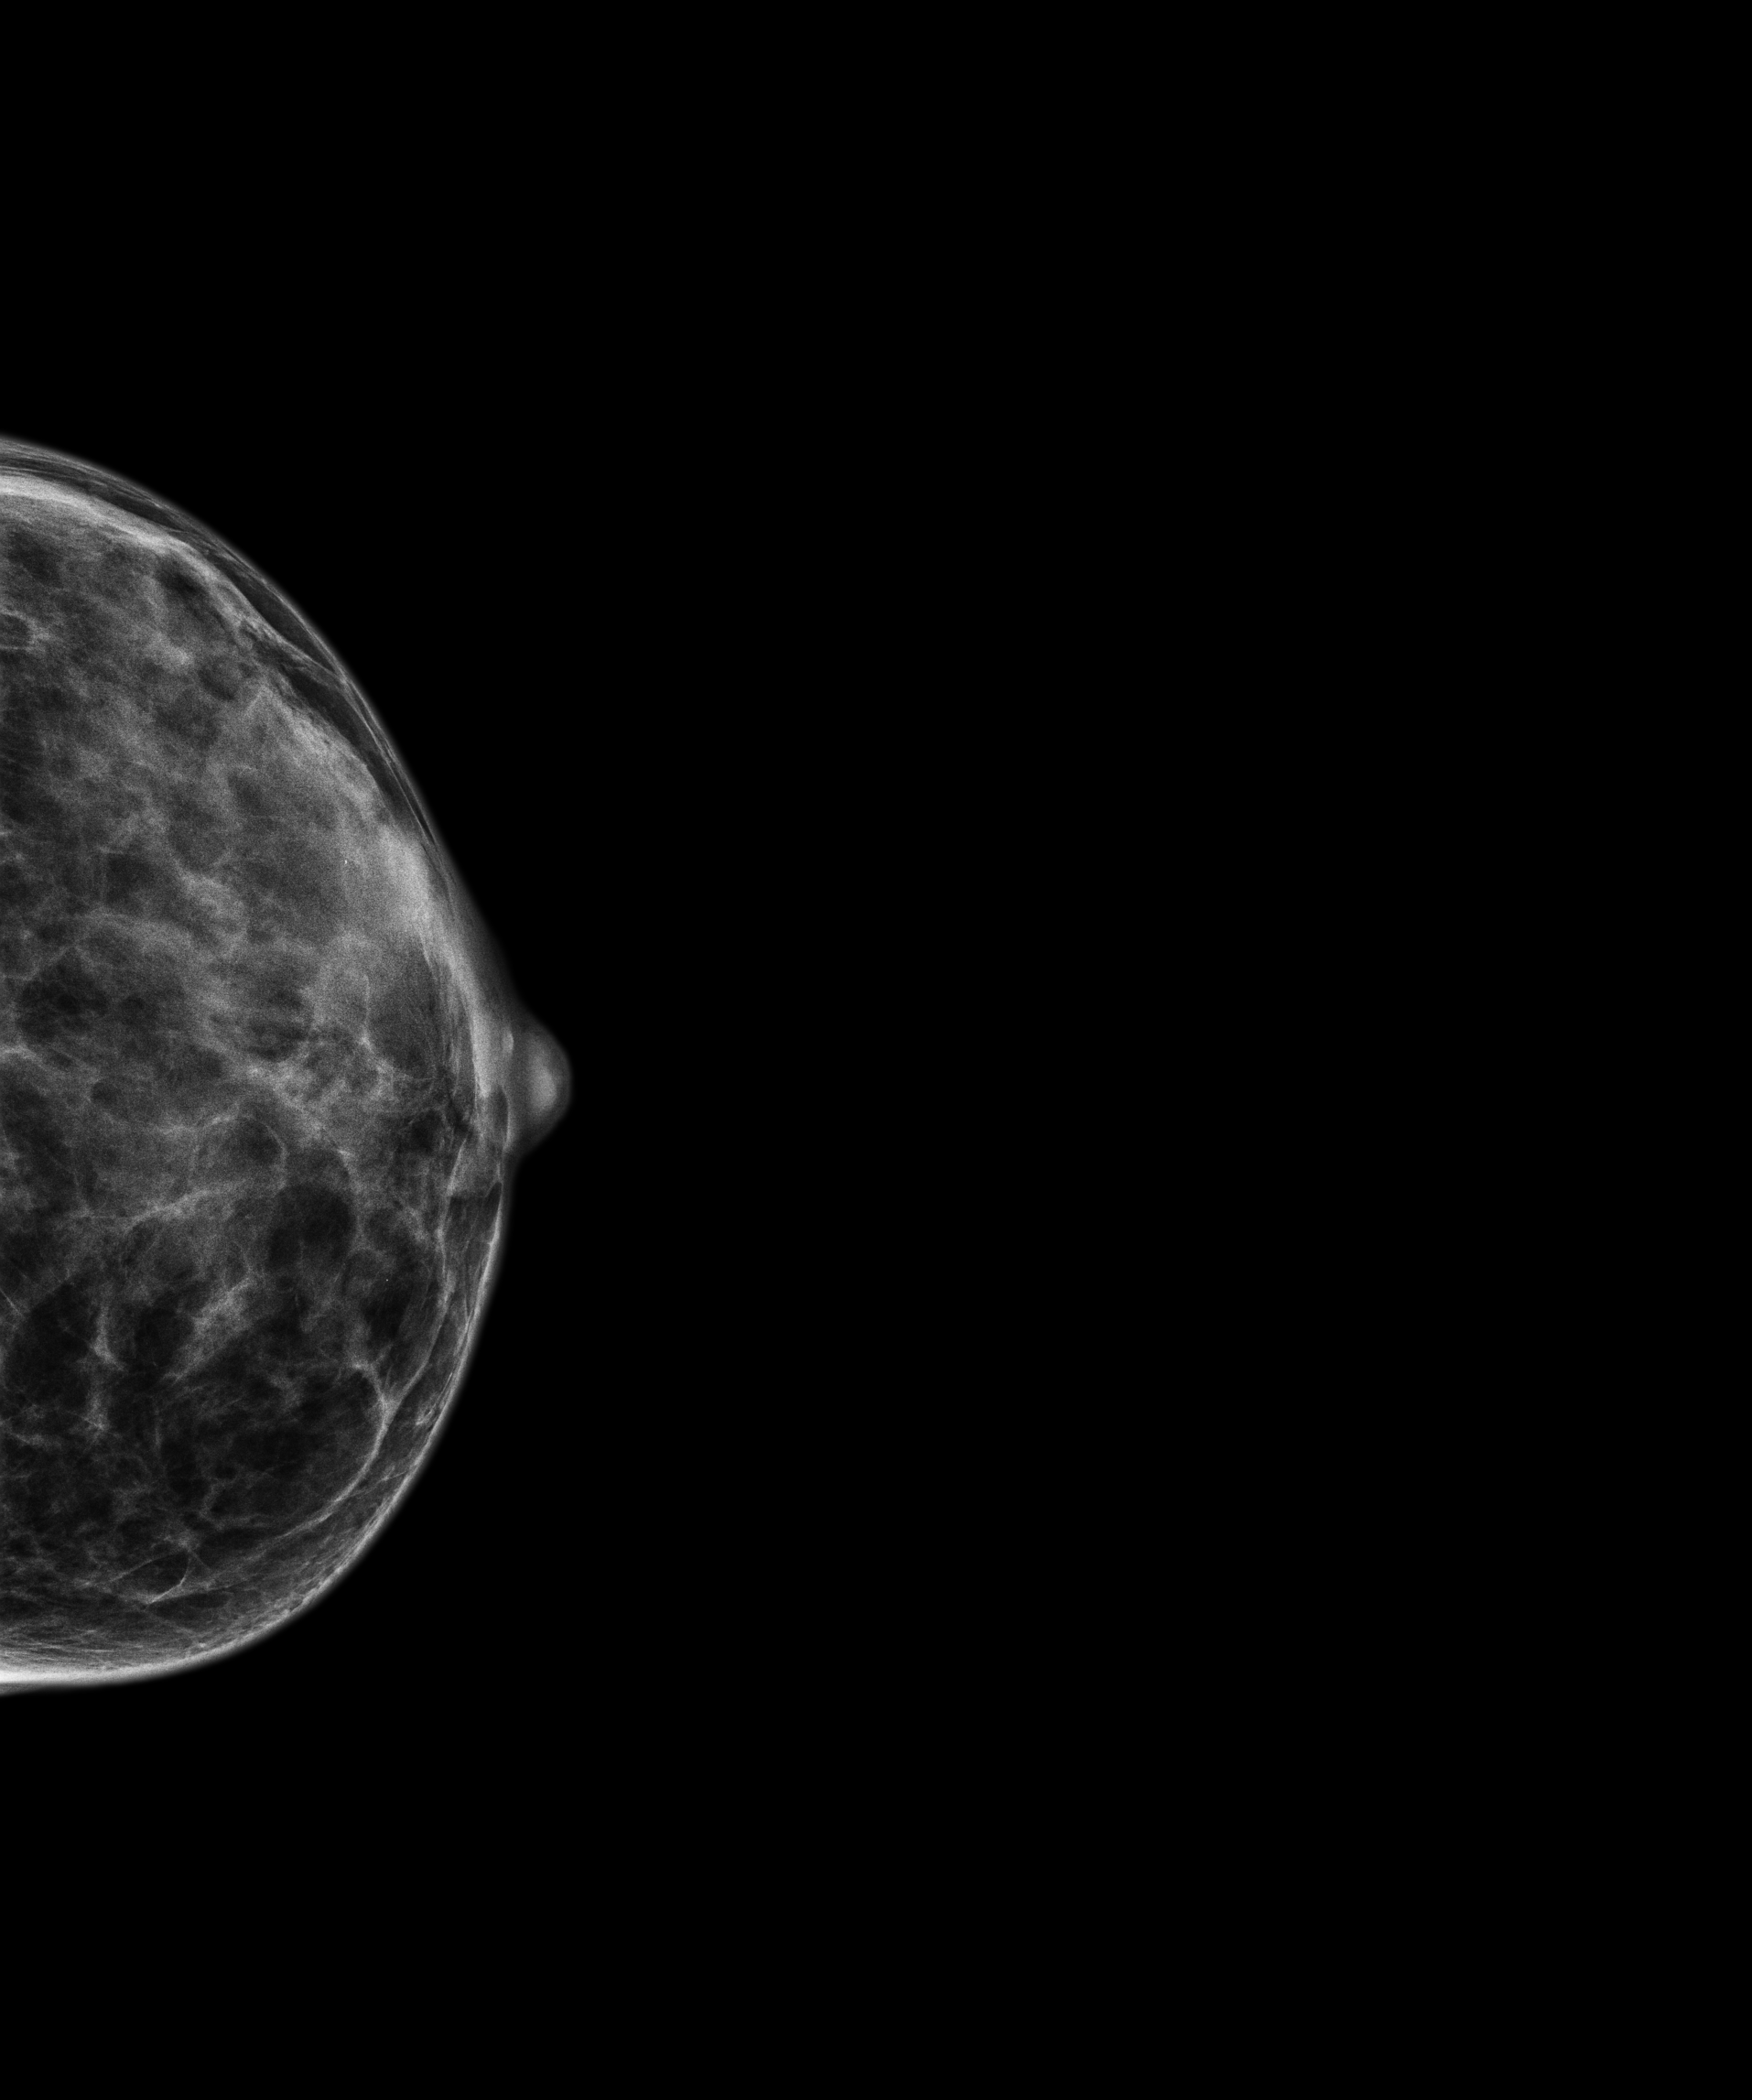
Annual screening mammography examination; compressed breast thickness 18.4 mm. Patient aged 54 years (female).
Image type: full-field digital mammogram. Breast: left. Projection: CC view. Breast density at the screening exam (both breasts): extremely dense (BI-RADS density category d). Final BI-RADS category for the screening round (tomosynthesis exam, both breasts): category 1. Recall: no recall after this screen.